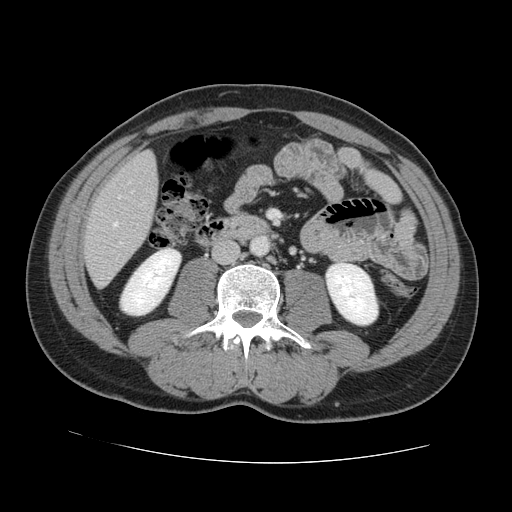
Contrast-enhanced abdominal CT, one axial slice; slice 32 of 131 in the series (ordered by position); intravenous contrast given; soft-tissue window (W 400 / L 40 HU); 512 × 512 image matrix, field of view 380 × 380 mm. Male patient, age 40 years. From the clinical record (not read from this slice): diagnosis: colorectal cancer liver metastases, imaged before liver resection; multiple liver metastases: yes; largest metastasis: 2.9 cm; chemotherapy before resection: yes.
Outlined on this slice (expert manual segmentation):
- hepatic veins: bounding box [x1, y1, x2, y2] px = [113, 182, 130, 227]
- liver: [85, 153, 158, 286]